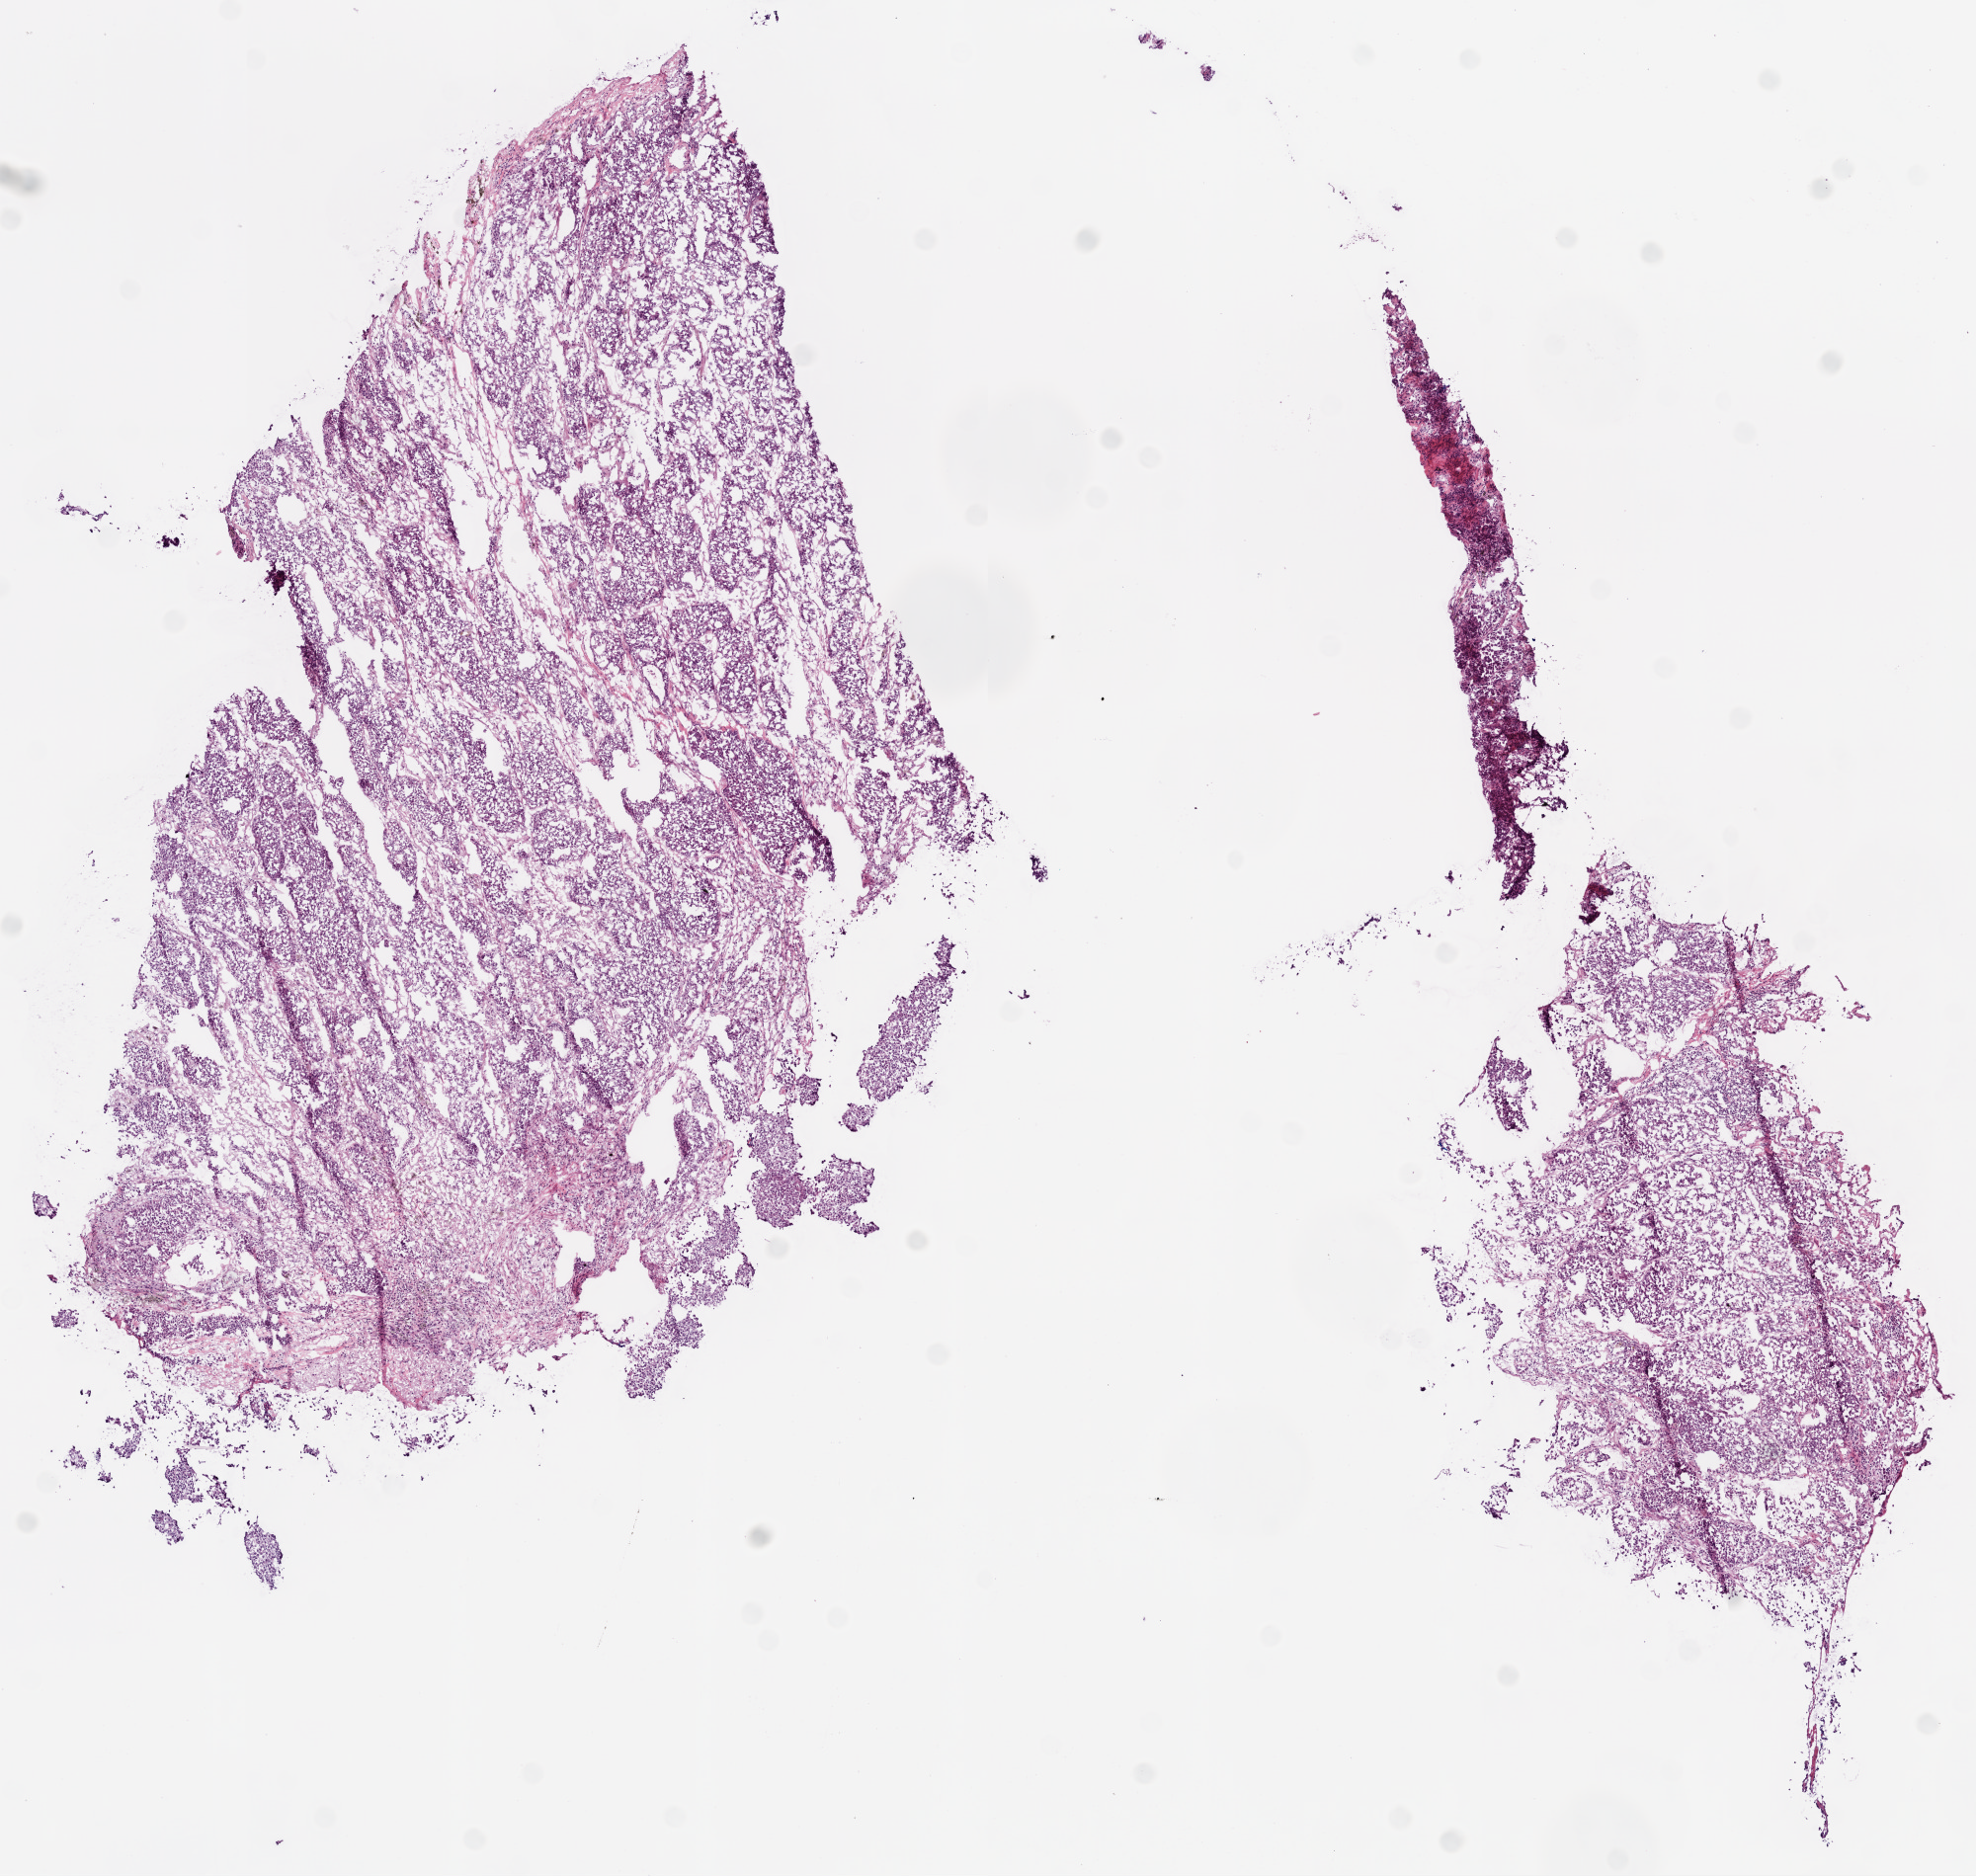
Whole-slide histology image, H&E, whole scanned area (about 8.0 x 7.6 mm) shown as a low-resolution overview, frozen section from the bottom of the tissue portion, sample: primary tumour, lung. Female patient; age at initial diagnosis 42 years. Pathologist review of this section (percent, as recorded): tumour cells 85%, tumour nuclei 80%.
Pathologic diagnosis: Adenocarcinoma, NOS (upper lobe, lung).